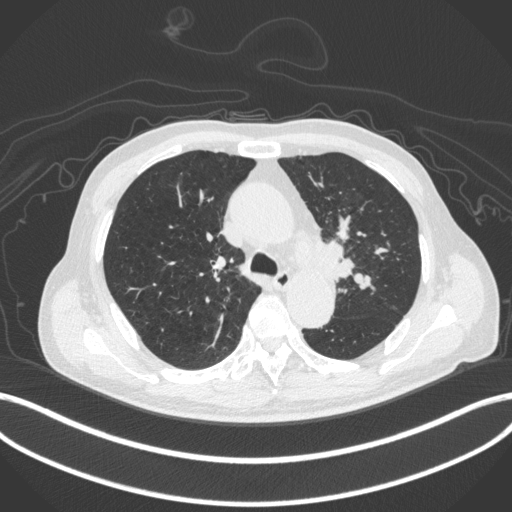
Chest CT, one axial slice; lung window (W 1500 / L -600 HU); 512 × 512 image matrix, field of view 400 × 400 mm. Patient: male, 77 years. From the clinical record (not read from this slice): clinical TNM (as recorded): T3 N1 M0.
Structures marked on this image (bounding box drawn by a radiologist):
- lung tumour (recorded histology: adenocarcinoma): bounding box <316,236,362,290> (left, top, right, bottom; pixels)